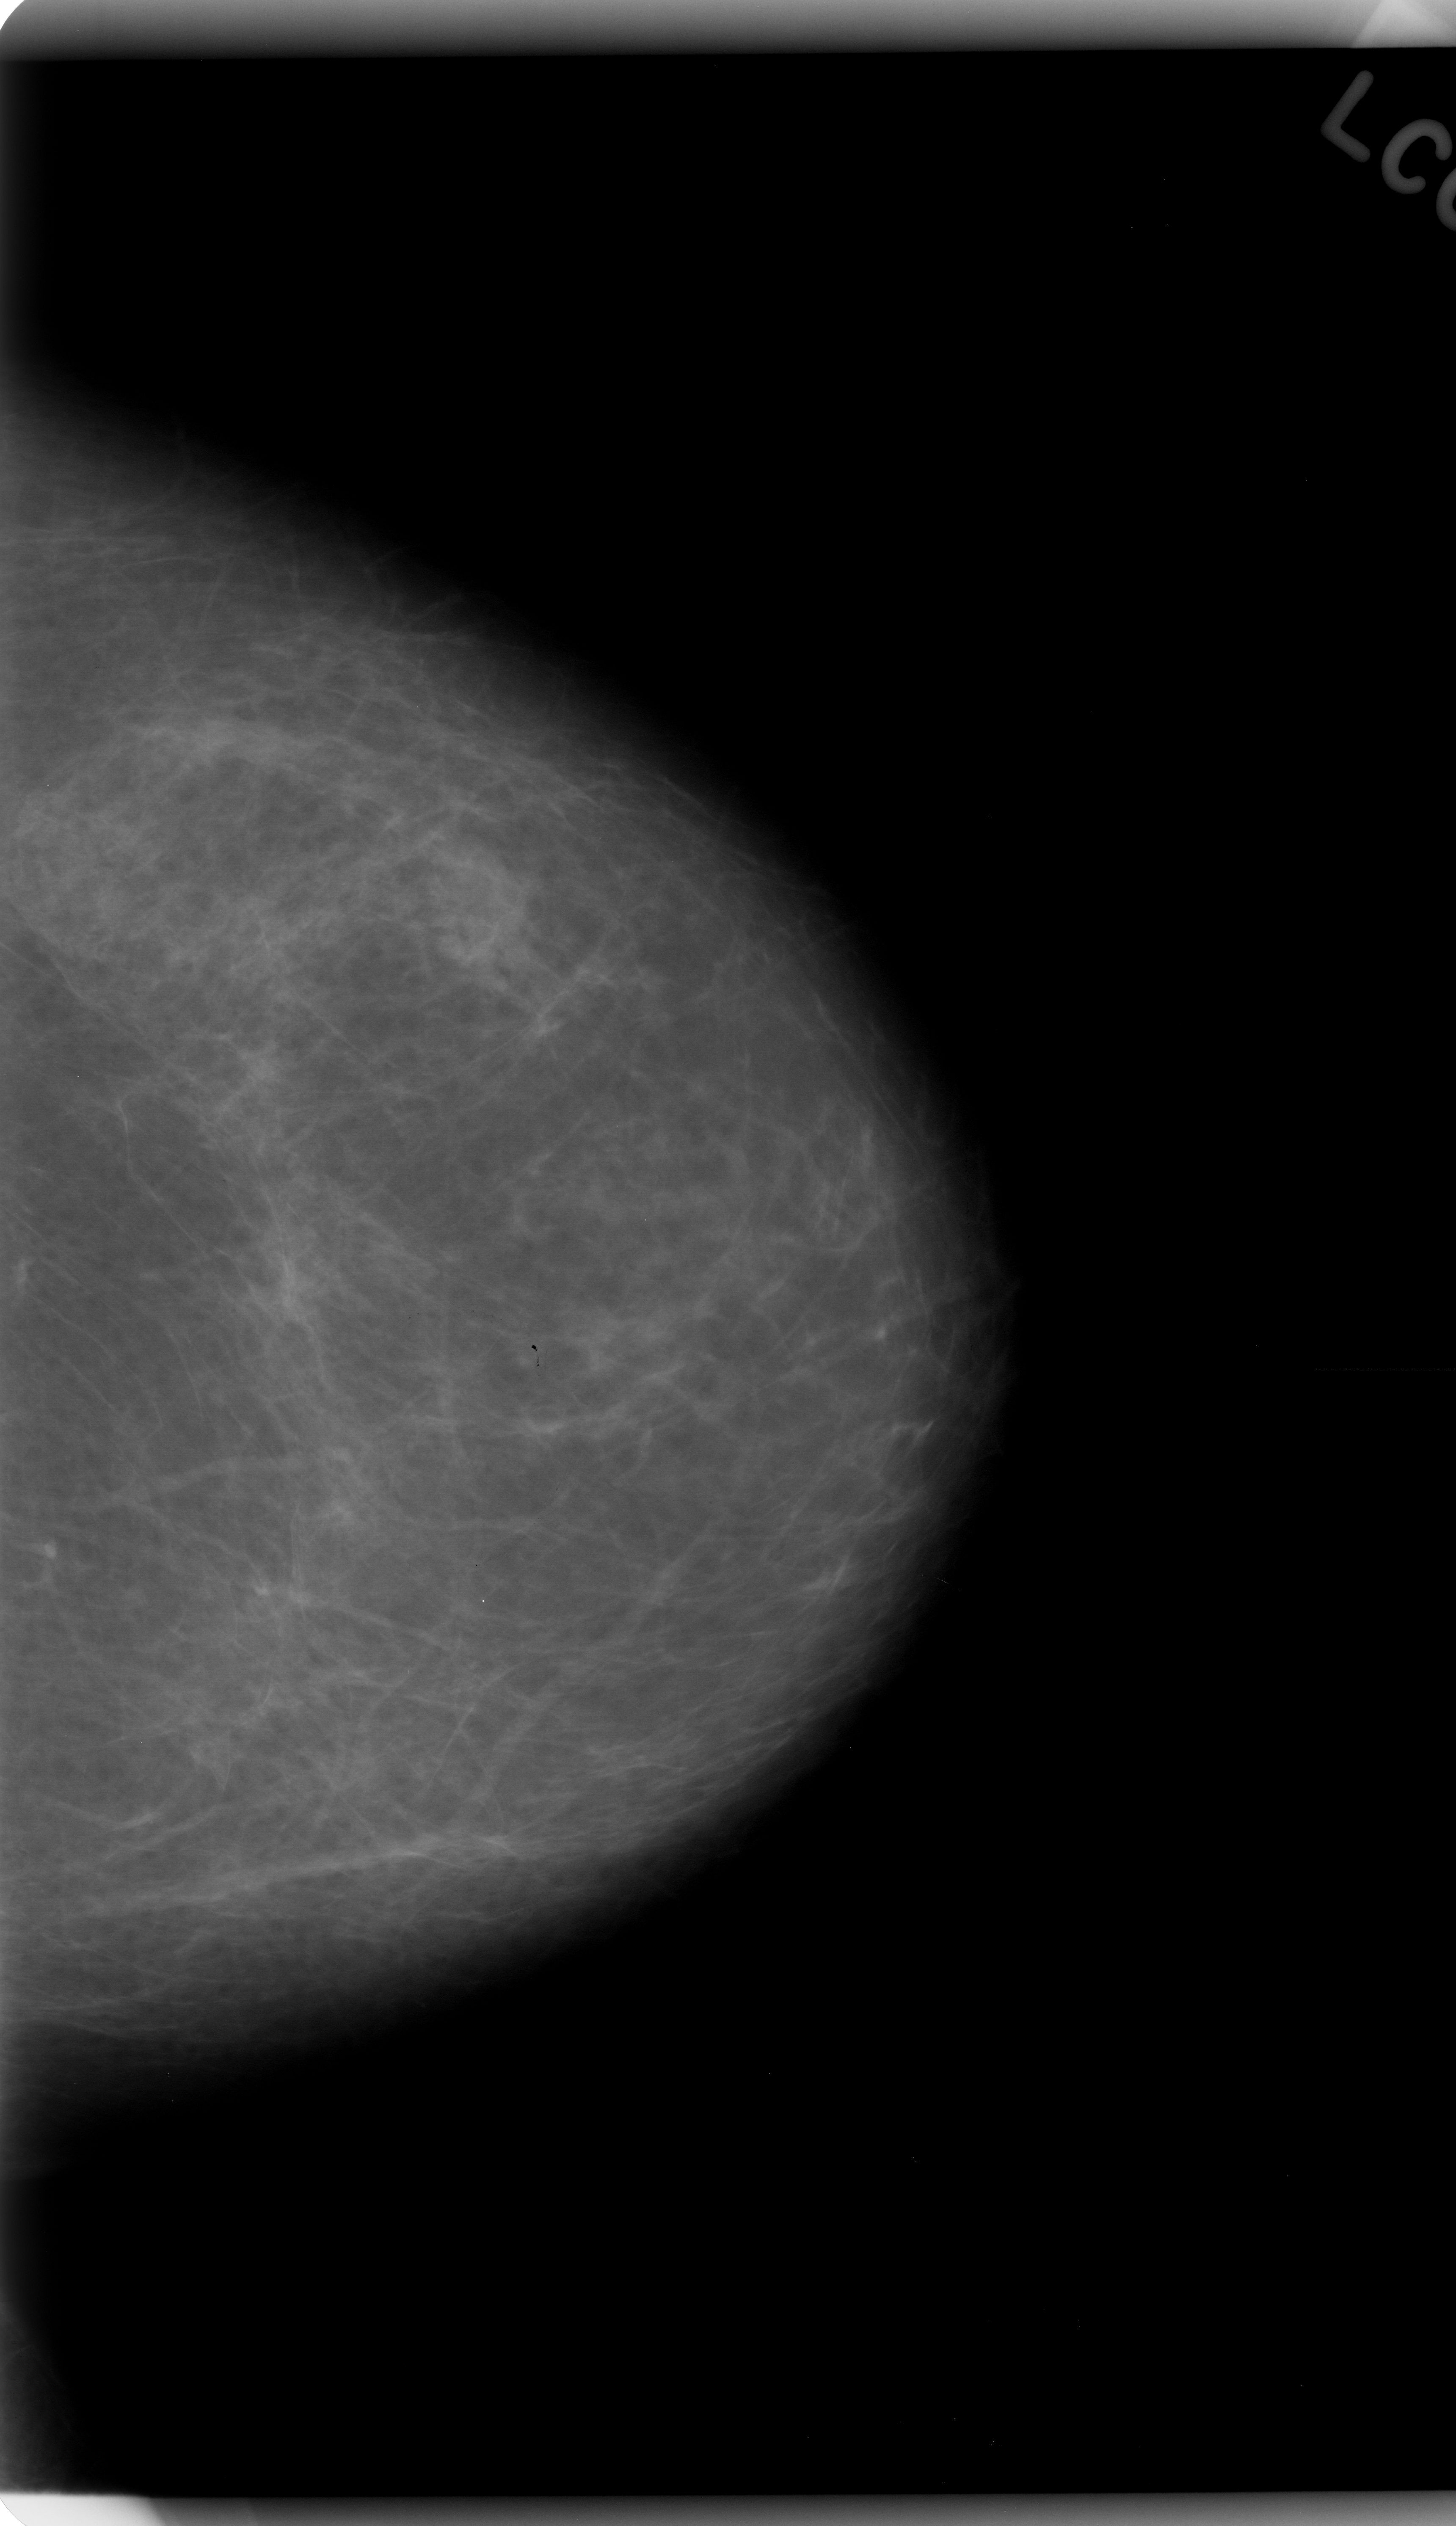
Scanned film-screen mammogram; left breast; CC view; BI-RADS breast density category 1 (scale 1–4); 1456 × 2526 image matrix.
Expert-marked regions of interest on this image (one box per marked abnormality):
- mass, shape oval, margins microlobulated; BI-RADS assessment category 4; subtlety rating 4 on a 1 (subtle) to 5 (obvious) scale; pathology result (as recorded, not read from the image): malignant: bounding box (x1, y1, x2, y2) in pixels: (426, 838, 532, 951)